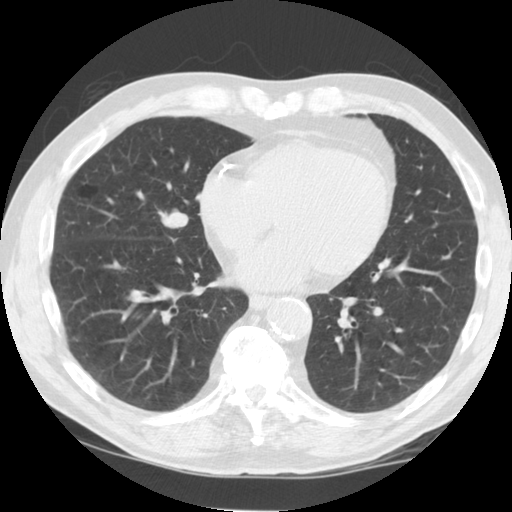
Axial slice from a low-dose chest CT screening exam, third annual screen, lung window (W 1500 / L -600 HU), slice 82 of 125 in the series, 512 × 512 image matrix, field of view 350 × 350 mm. Male participant, aged 64 years at enrolment.
- Expert-annotated lung lesion, bounding box <135,196,199,250> (left, top, right, bottom; pixels).
- Reader record for this screening exam (exam-level; its link to the box is not recorded): non-calcified nodule or mass ≥4 mm, right middle lobe, 21 × 14 mm, smooth margins, soft tissue attenuation, pre-existing on the prior screen: yes; interval growth: yes.
- Later outcome: lung cancer diagnosed 74 days after this screen — non-small cell carcinoma, right middle lobe, poorly differentiated (G3), stage IIIA (AJCC 6th edition), 20 mm at pathology.